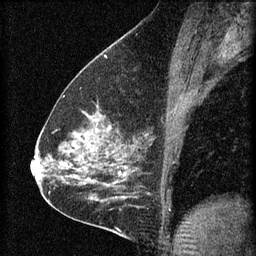
Breast MRI (dynamic contrast-enhanced), one sagittal slice; slice 37 of 60 in the series (ordered by position); 3 images stored at this slice position (order not interpretable as contrast timing); 1.5 T; TE 4.2 ms, TR 8.2 ms; 2 mm slice thickness; 256 × 256 image matrix. Female patient, age 59 years.
Structures marked on this image (semi-automatic segmentation, software-assisted and operator-edited):
- analysis volume of interest (the breast-tissue region the enhancement analysis was run in; not a lesion): bounding box (x1, y1, x2, y2) in pixels: (61, 104, 134, 161)
- tumour enhancement mask (voxels above the 70 % enhancement threshold inside the analysis volume of interest): (72, 120, 112, 149)